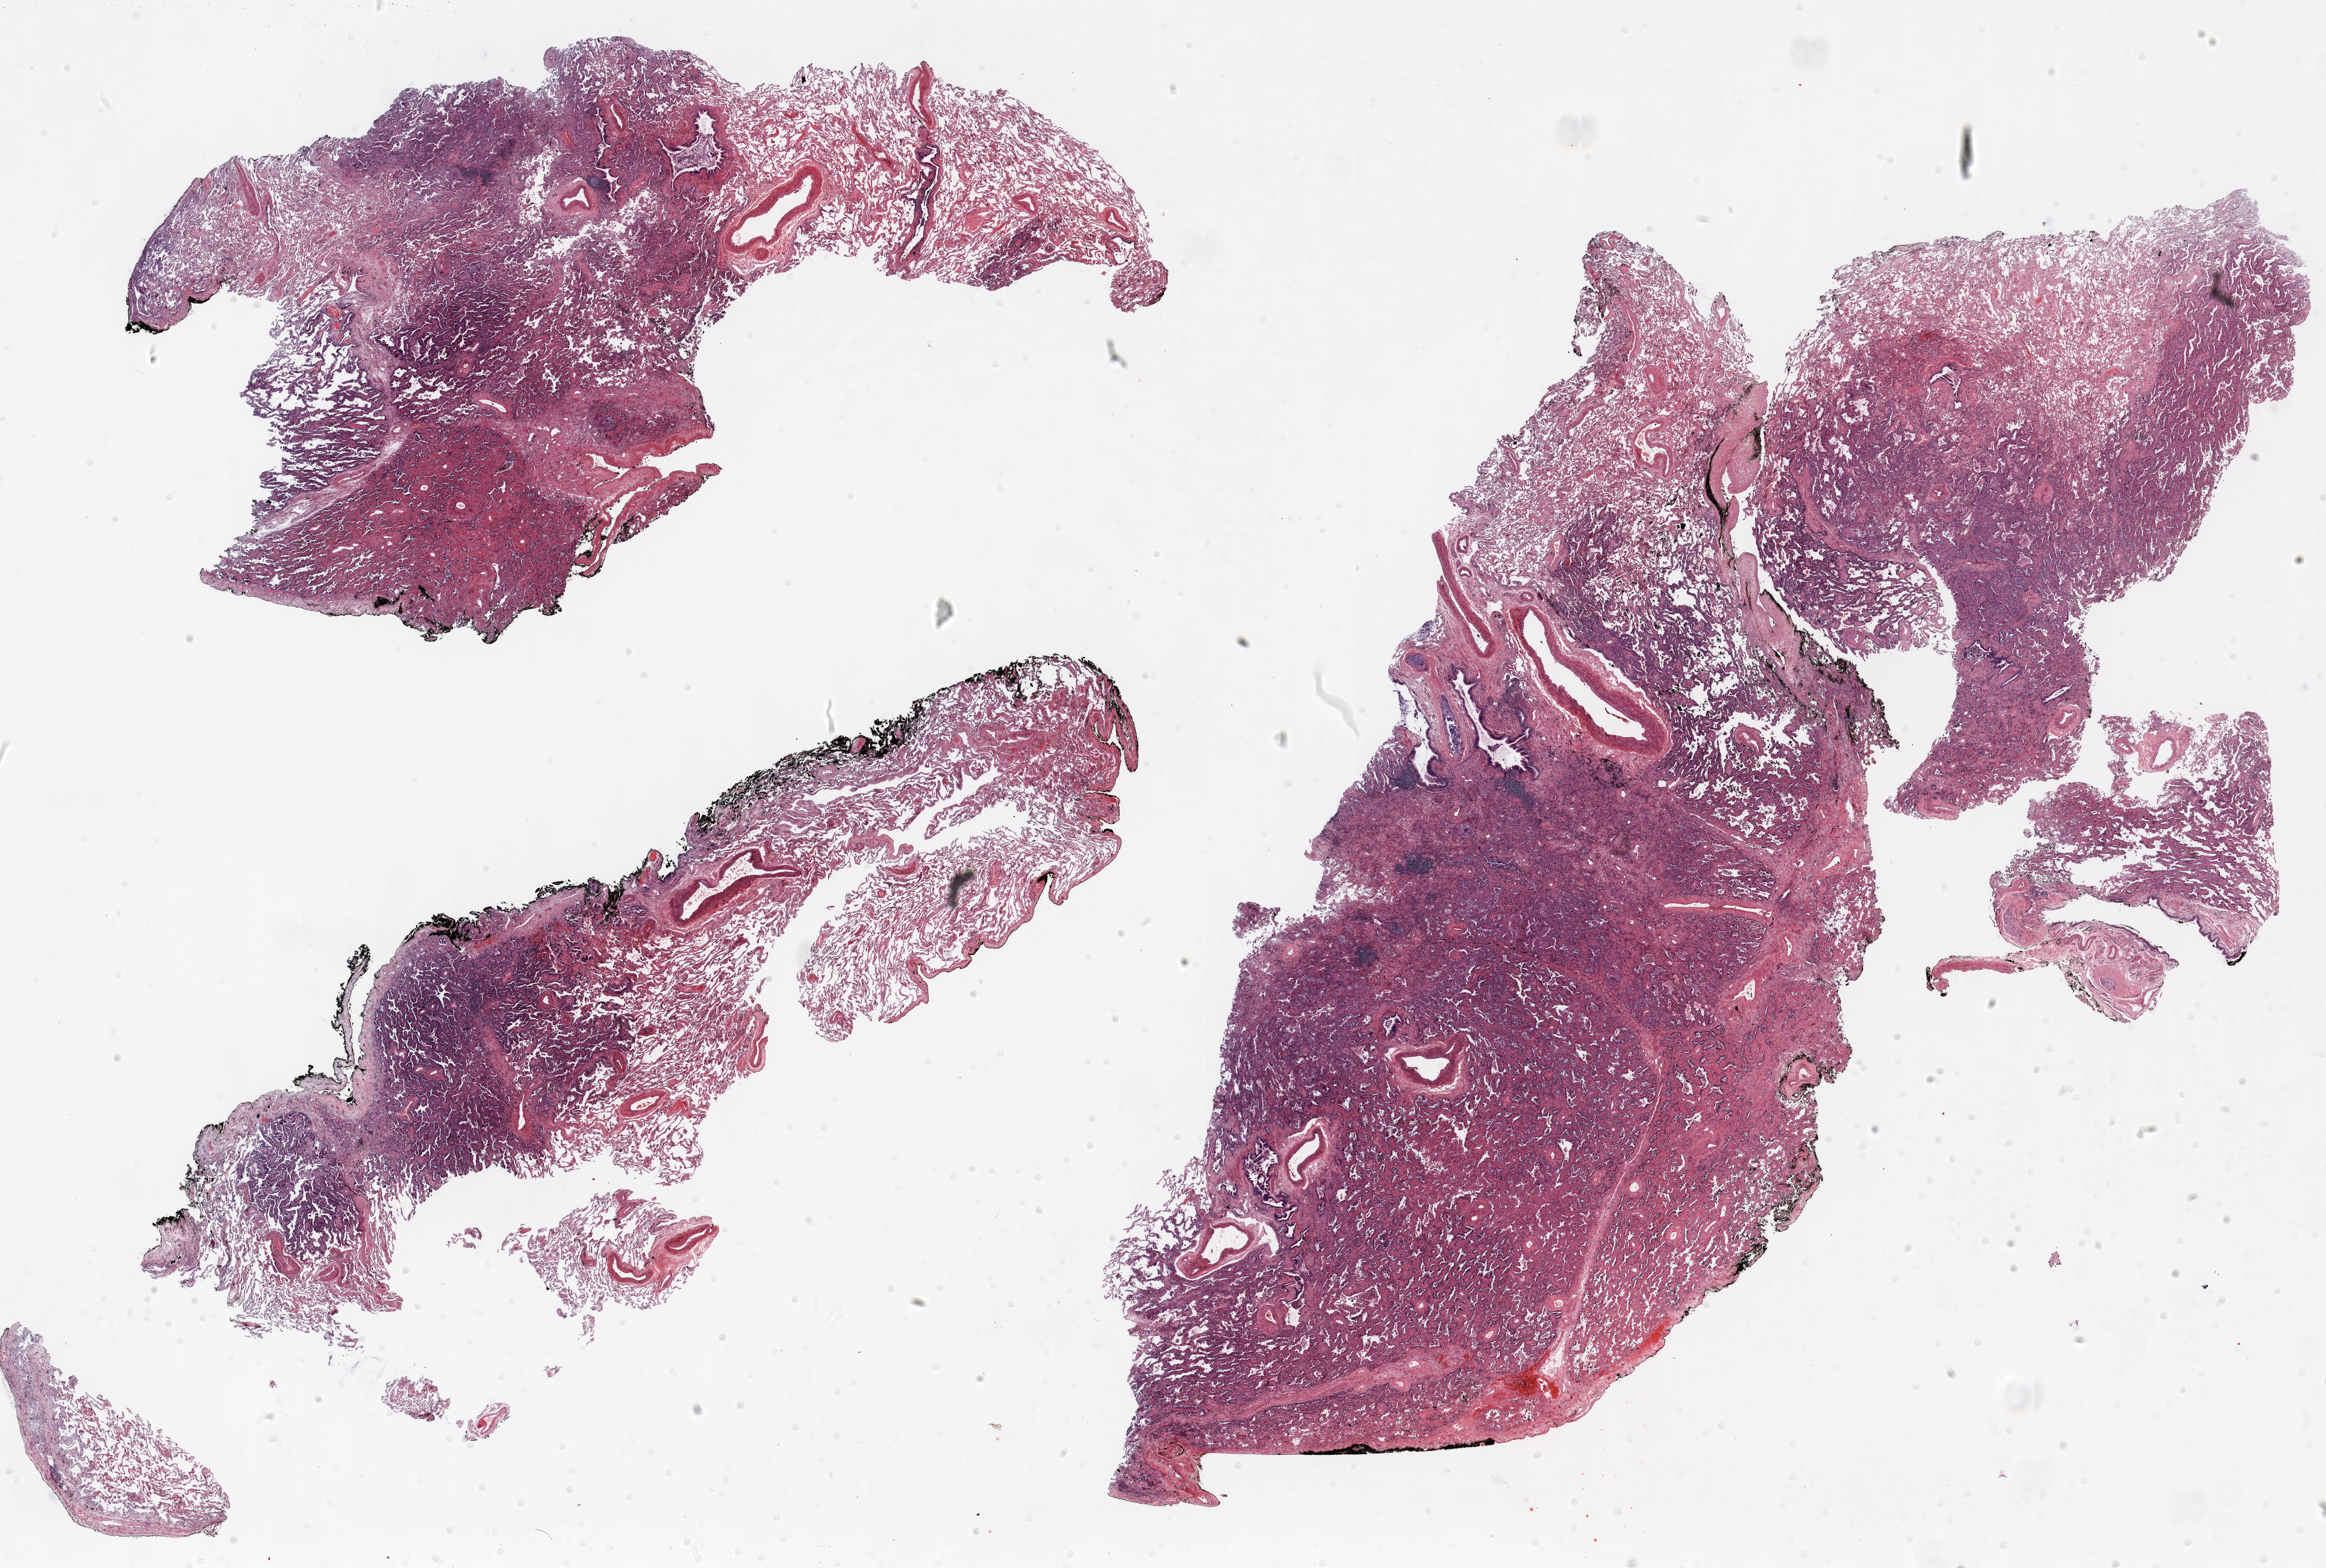
Whole-slide histology image, H&E, a low-resolution overview of the entire scanned area, about 31.0 x 20.9 mm, FFPE section, lung. Male, age 63 at enrolment. Former smoker at enrolment. Grade: moderately differentiated (G2).
Stage (AJCC 6th edition): IA. Participant's lung-cancer diagnosis: Adenocarcinoma, NOS (ICD-O-3 8140/3). Primary tumour location (clinical record): left upper lobe. Tumour size (pathology): 14 mm.